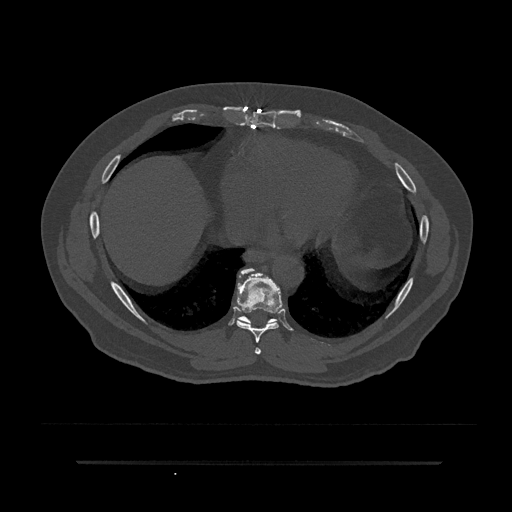
CT including the spine, one axial slice. Slice 412 of 797 in the series (ordered by position). Reconstruction kernel Br40s/3. Bone window (W 1800 / L 400 HU). 512 × 512 image matrix, field of view 464 × 464 mm. Patient: male, 59 years. Case-level facts recorded for this patient, not image findings: primary cancer: bile ducts.
Structures marked on this image (semi-automatic segmentation, software-assisted and operator-edited):
- T7 vertebra: bounding box <255,347,261,354> (left, top, right, bottom; pixels)
- T8 vertebra: <235,268,283,355>
- T9 vertebra: <237,268,277,325>